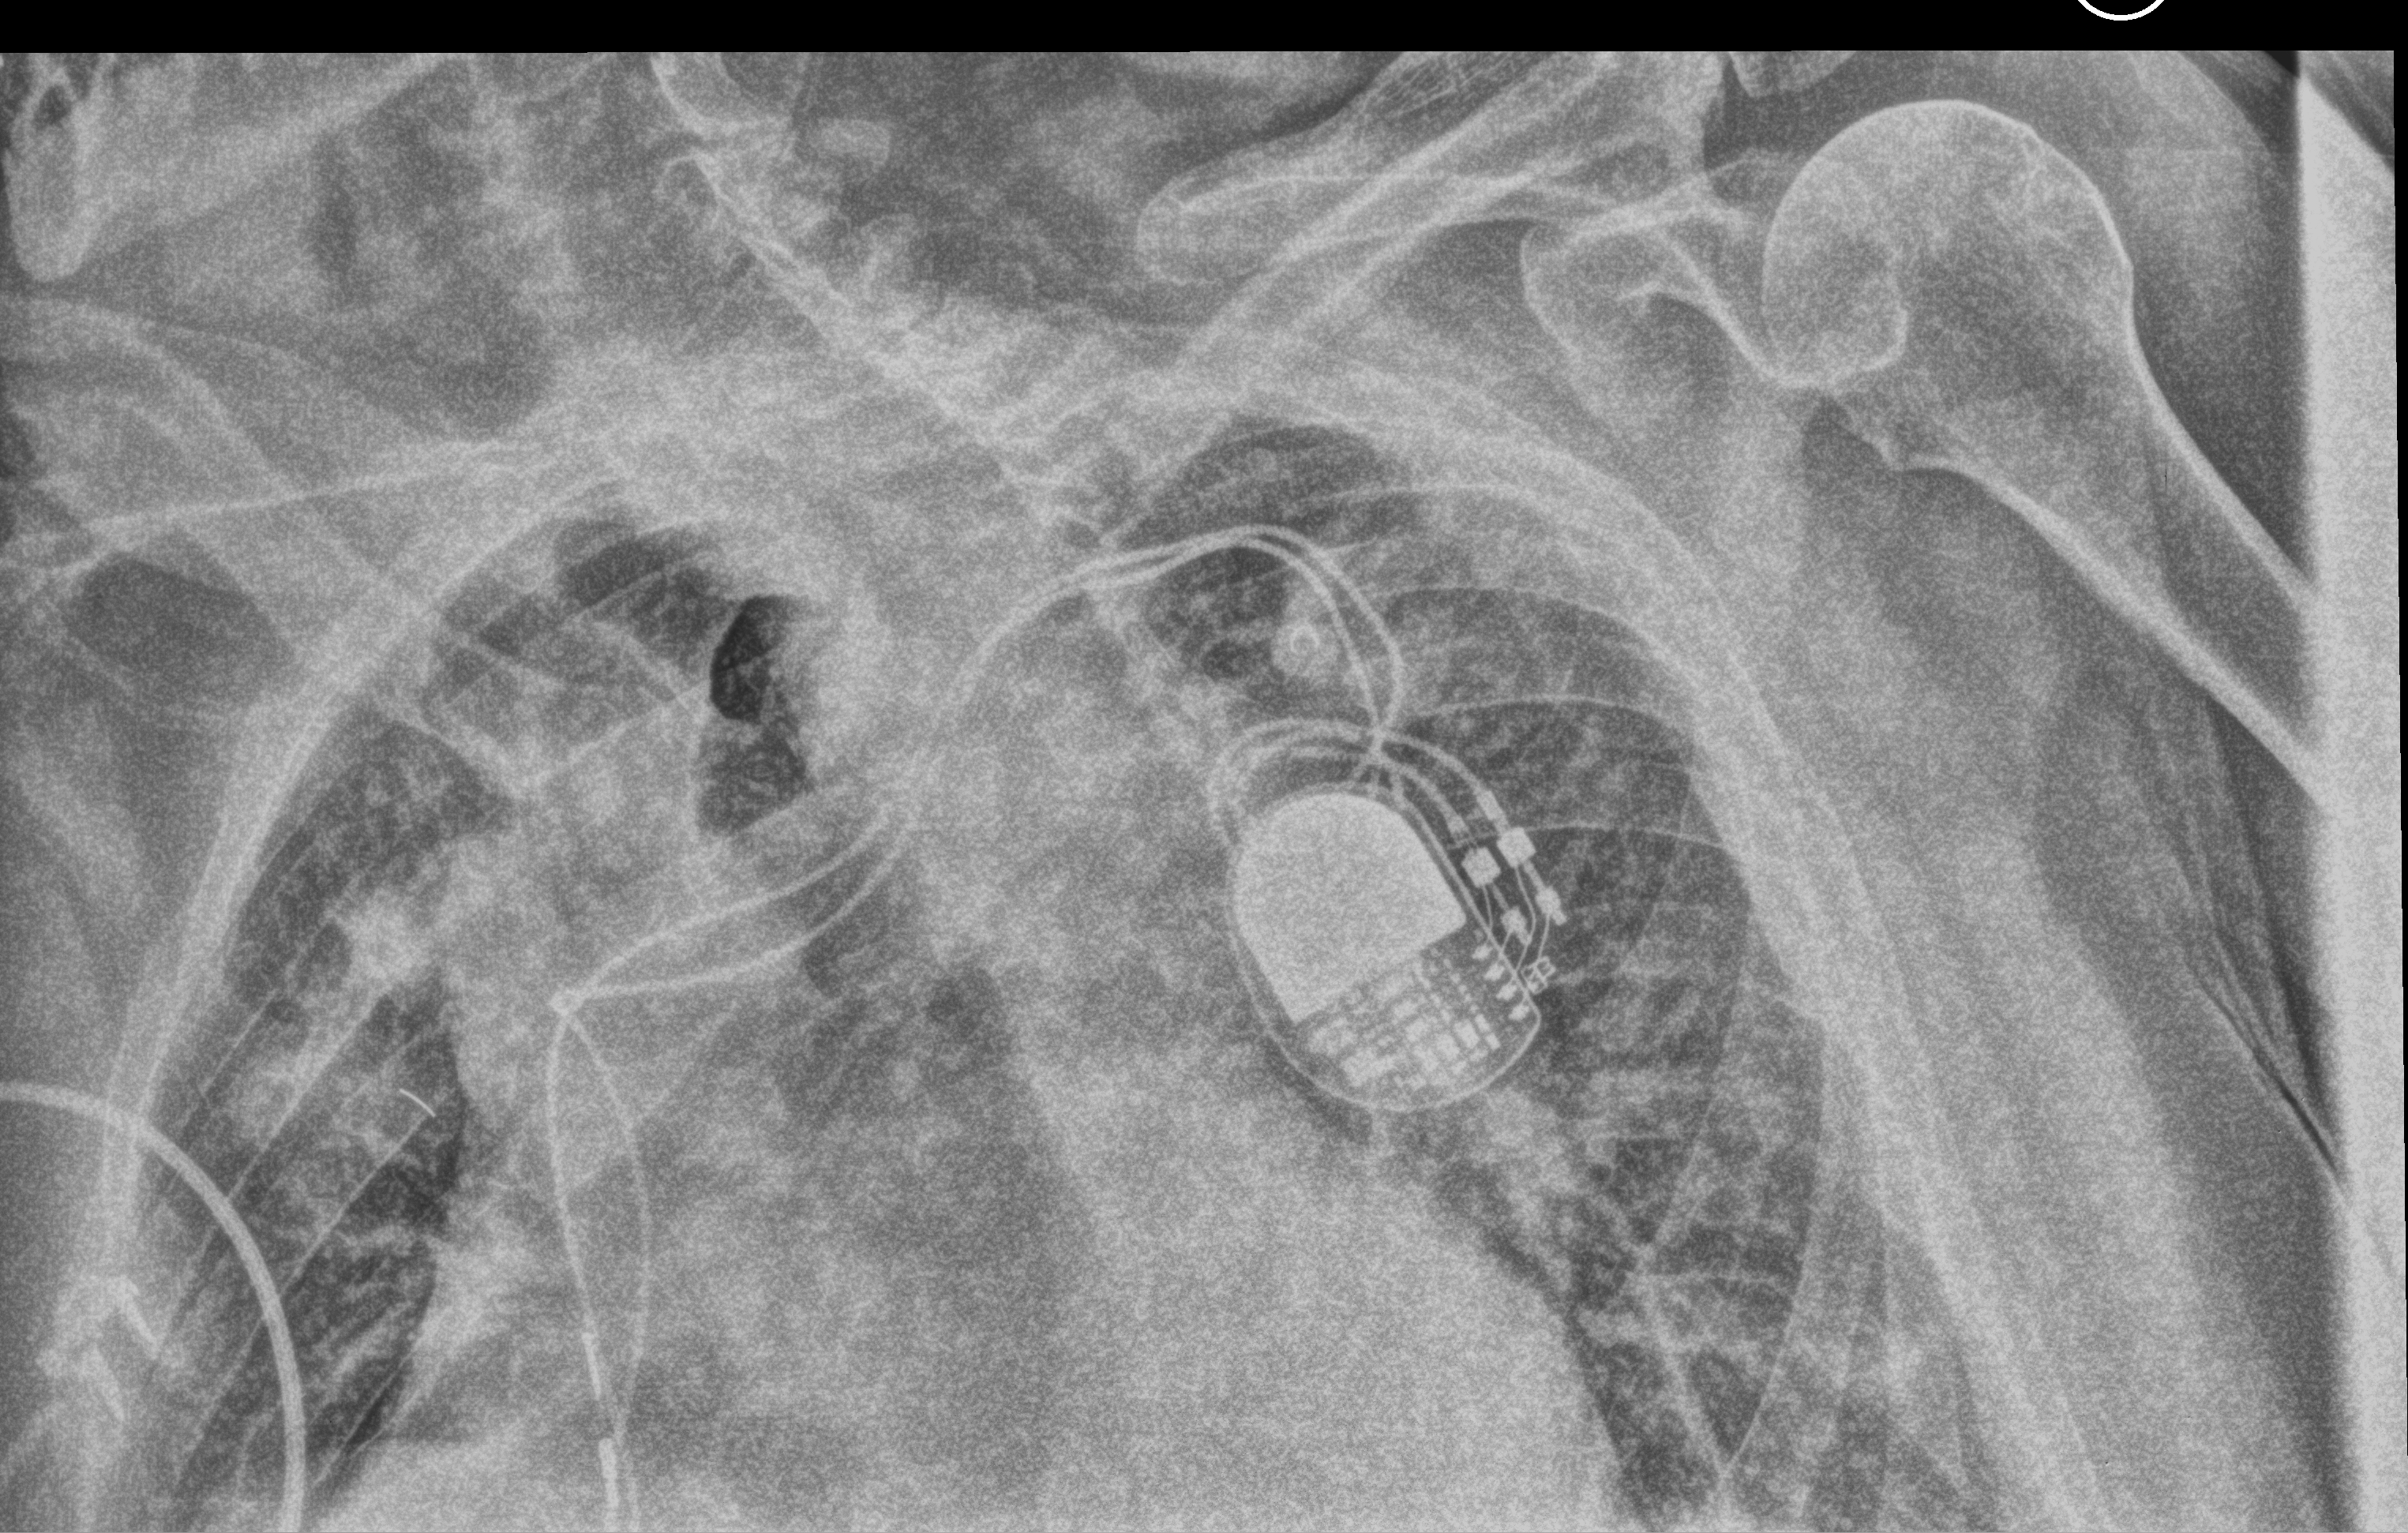
Chest X-ray (portable); anteroposterior (AP) projection. Patient hospitalised with COVID-19; male, aged 75–90 years.
Hospital-stay facts (about this admission, not read from this image; timing relative to this image not recorded): admitted to intensive care during this hospital stay: no; diabetes (admission record): no; mechanically ventilated during this hospital stay: no.